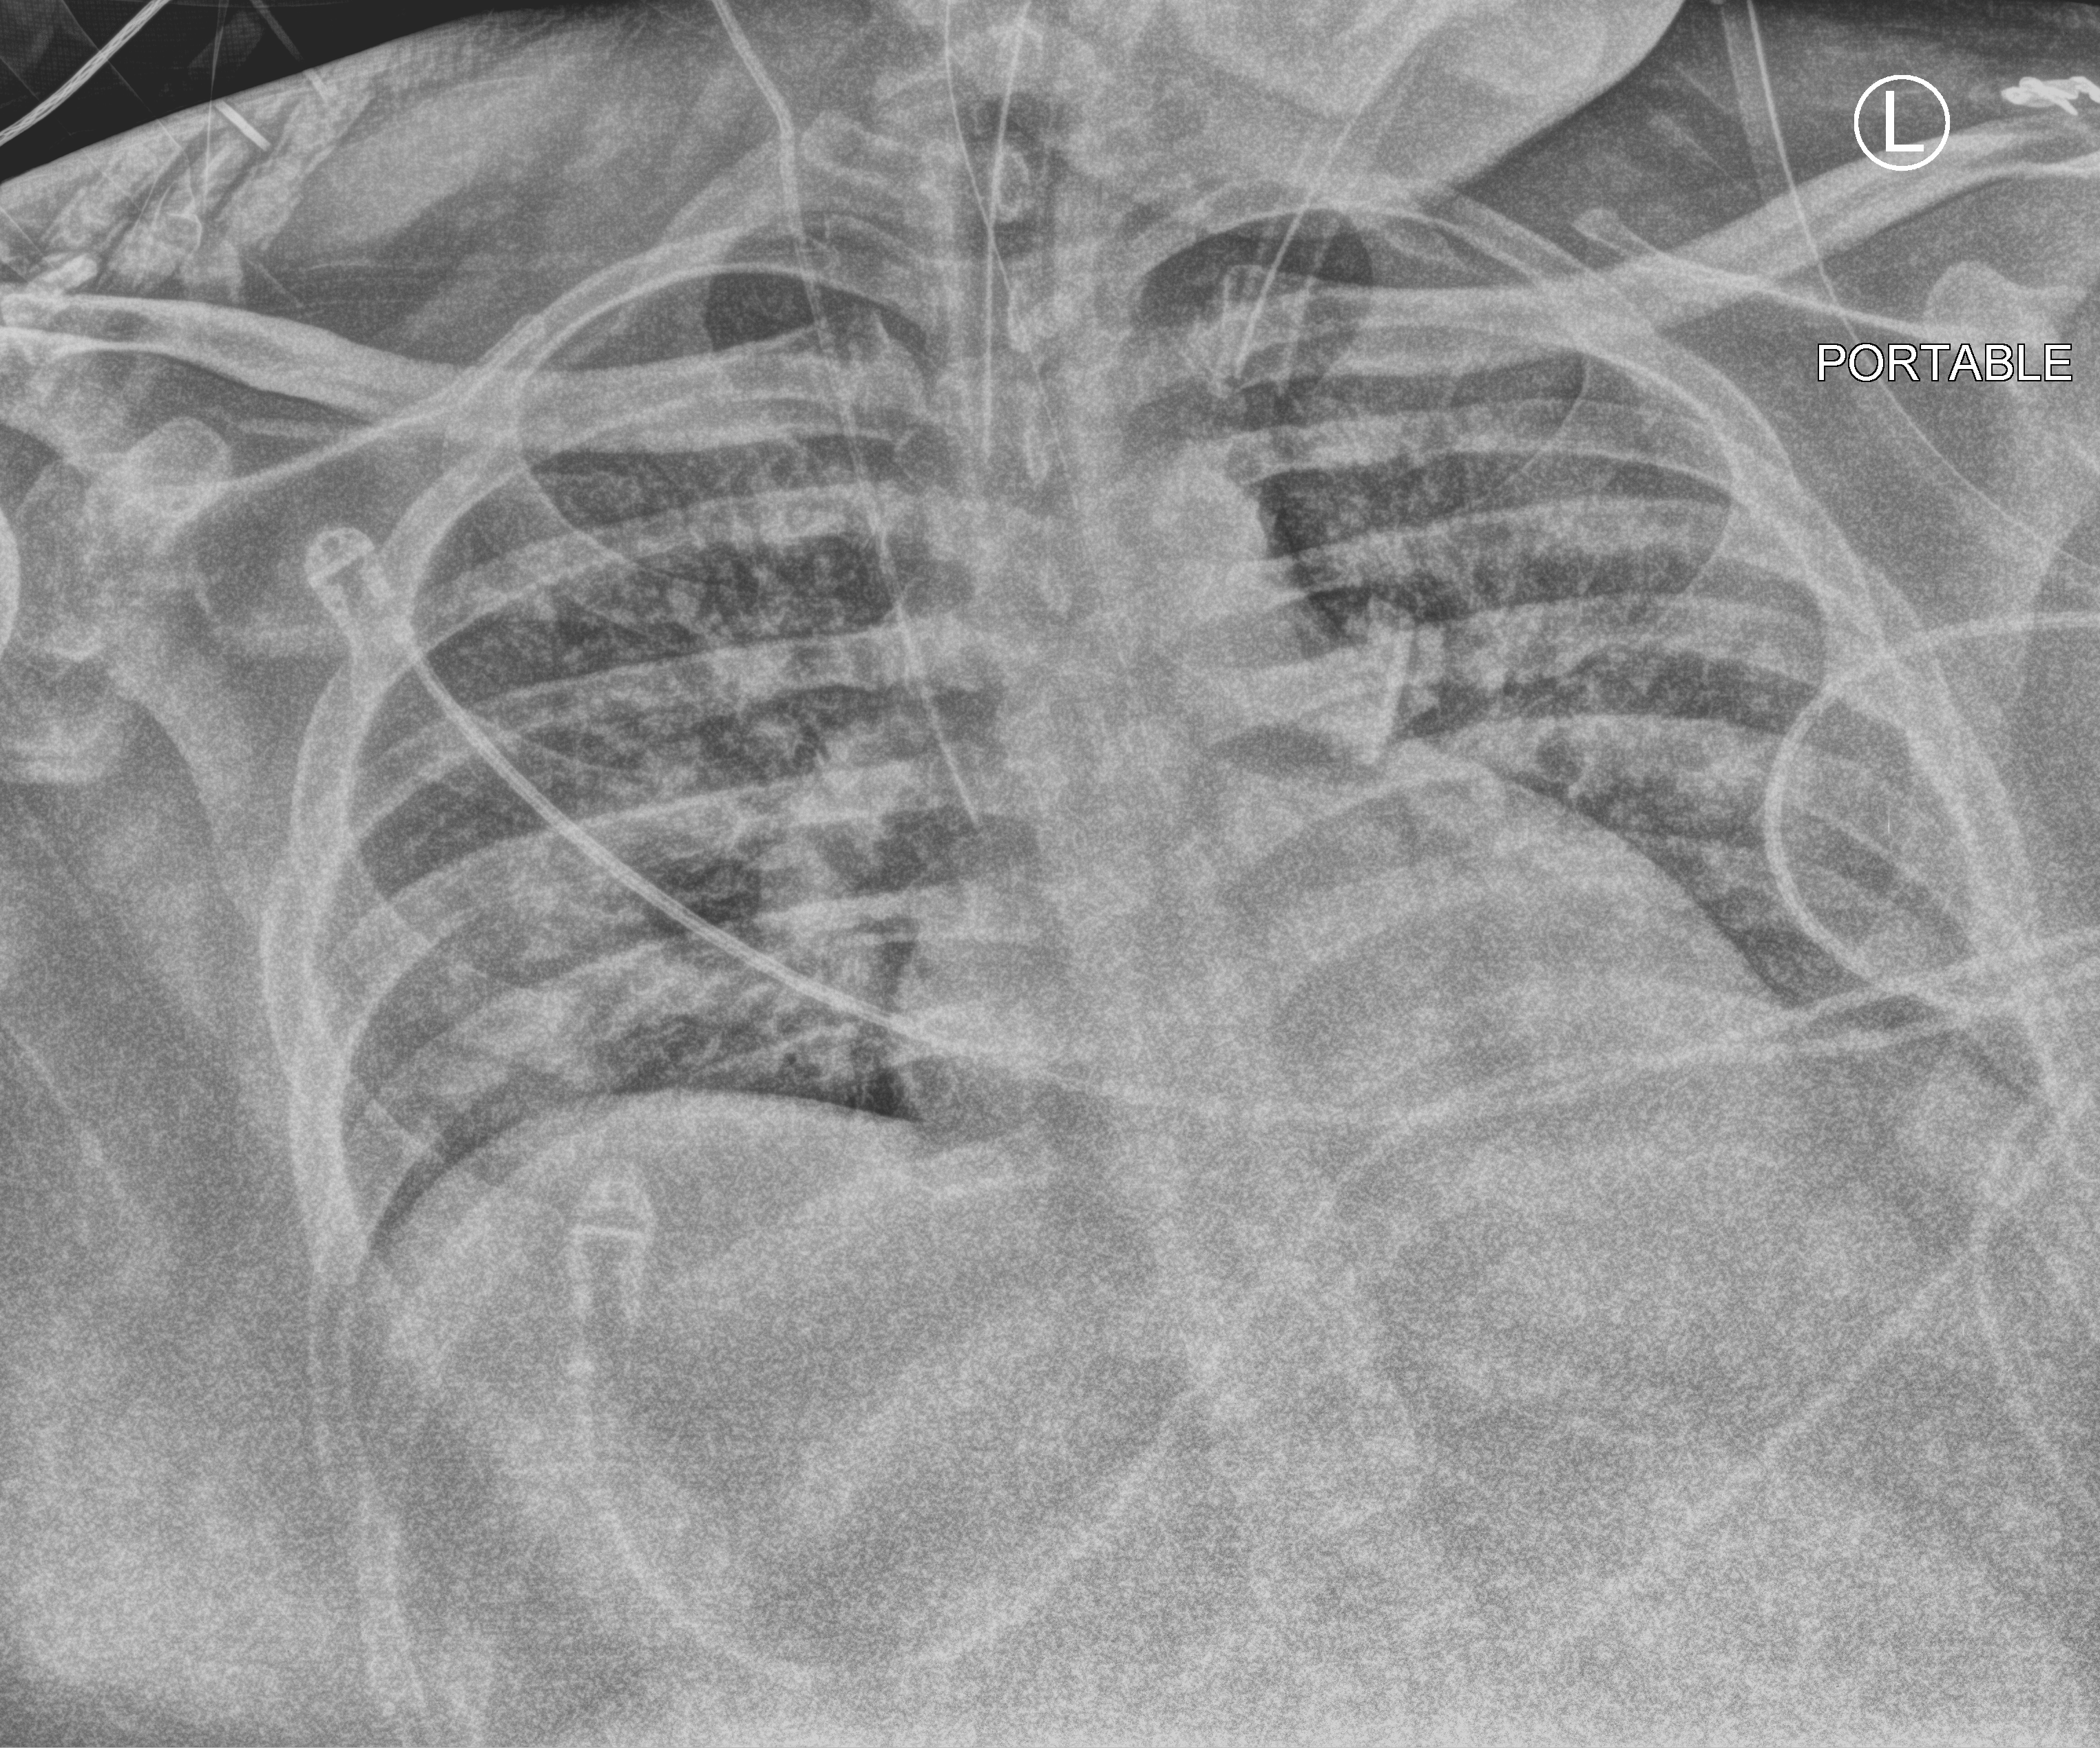
Bedside chest radiograph (computed radiography), anteroposterior (AP) projection. Patient hospitalised with COVID-19; male, aged 18–59 years.
Admission-level facts for this patient (not findings on this image; timing relative to this image not recorded): other chronic lung disease (admission record): yes; admitted to intensive care during this hospital stay: yes; mechanically ventilated during this hospital stay: yes.